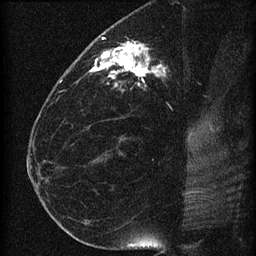
Breast MRI (dynamic contrast-enhanced), one sagittal slice; slice 31 of 60 in the series (ordered by position); dynamic contrast-enhanced series, image 2 of 4 at this slice position (ordered by acquisition); 1.5 T; TE 4.2 ms, TR 22.7 ms; 1.5 mm slice thickness; 256 × 256 image matrix, field of view 180 × 180 mm. Patient: female, 35 years. From the clinical record (not read from this slice): setting: breast cancer imaged before/during neoadjuvant chemotherapy; receptor status: HR-positive, HER2-negative.
Outlined on this slice (semi-automatically segmented with operator editing):
- analysis volume of interest (the breast-tissue region the enhancement analysis was run in; not a lesion): box from (x=69, y=27) to (x=198, y=112) px
- tumour enhancement mask (voxels above the 90 % enhancement threshold inside the analysis volume of interest): (x=88, y=37)–(x=166, y=91)